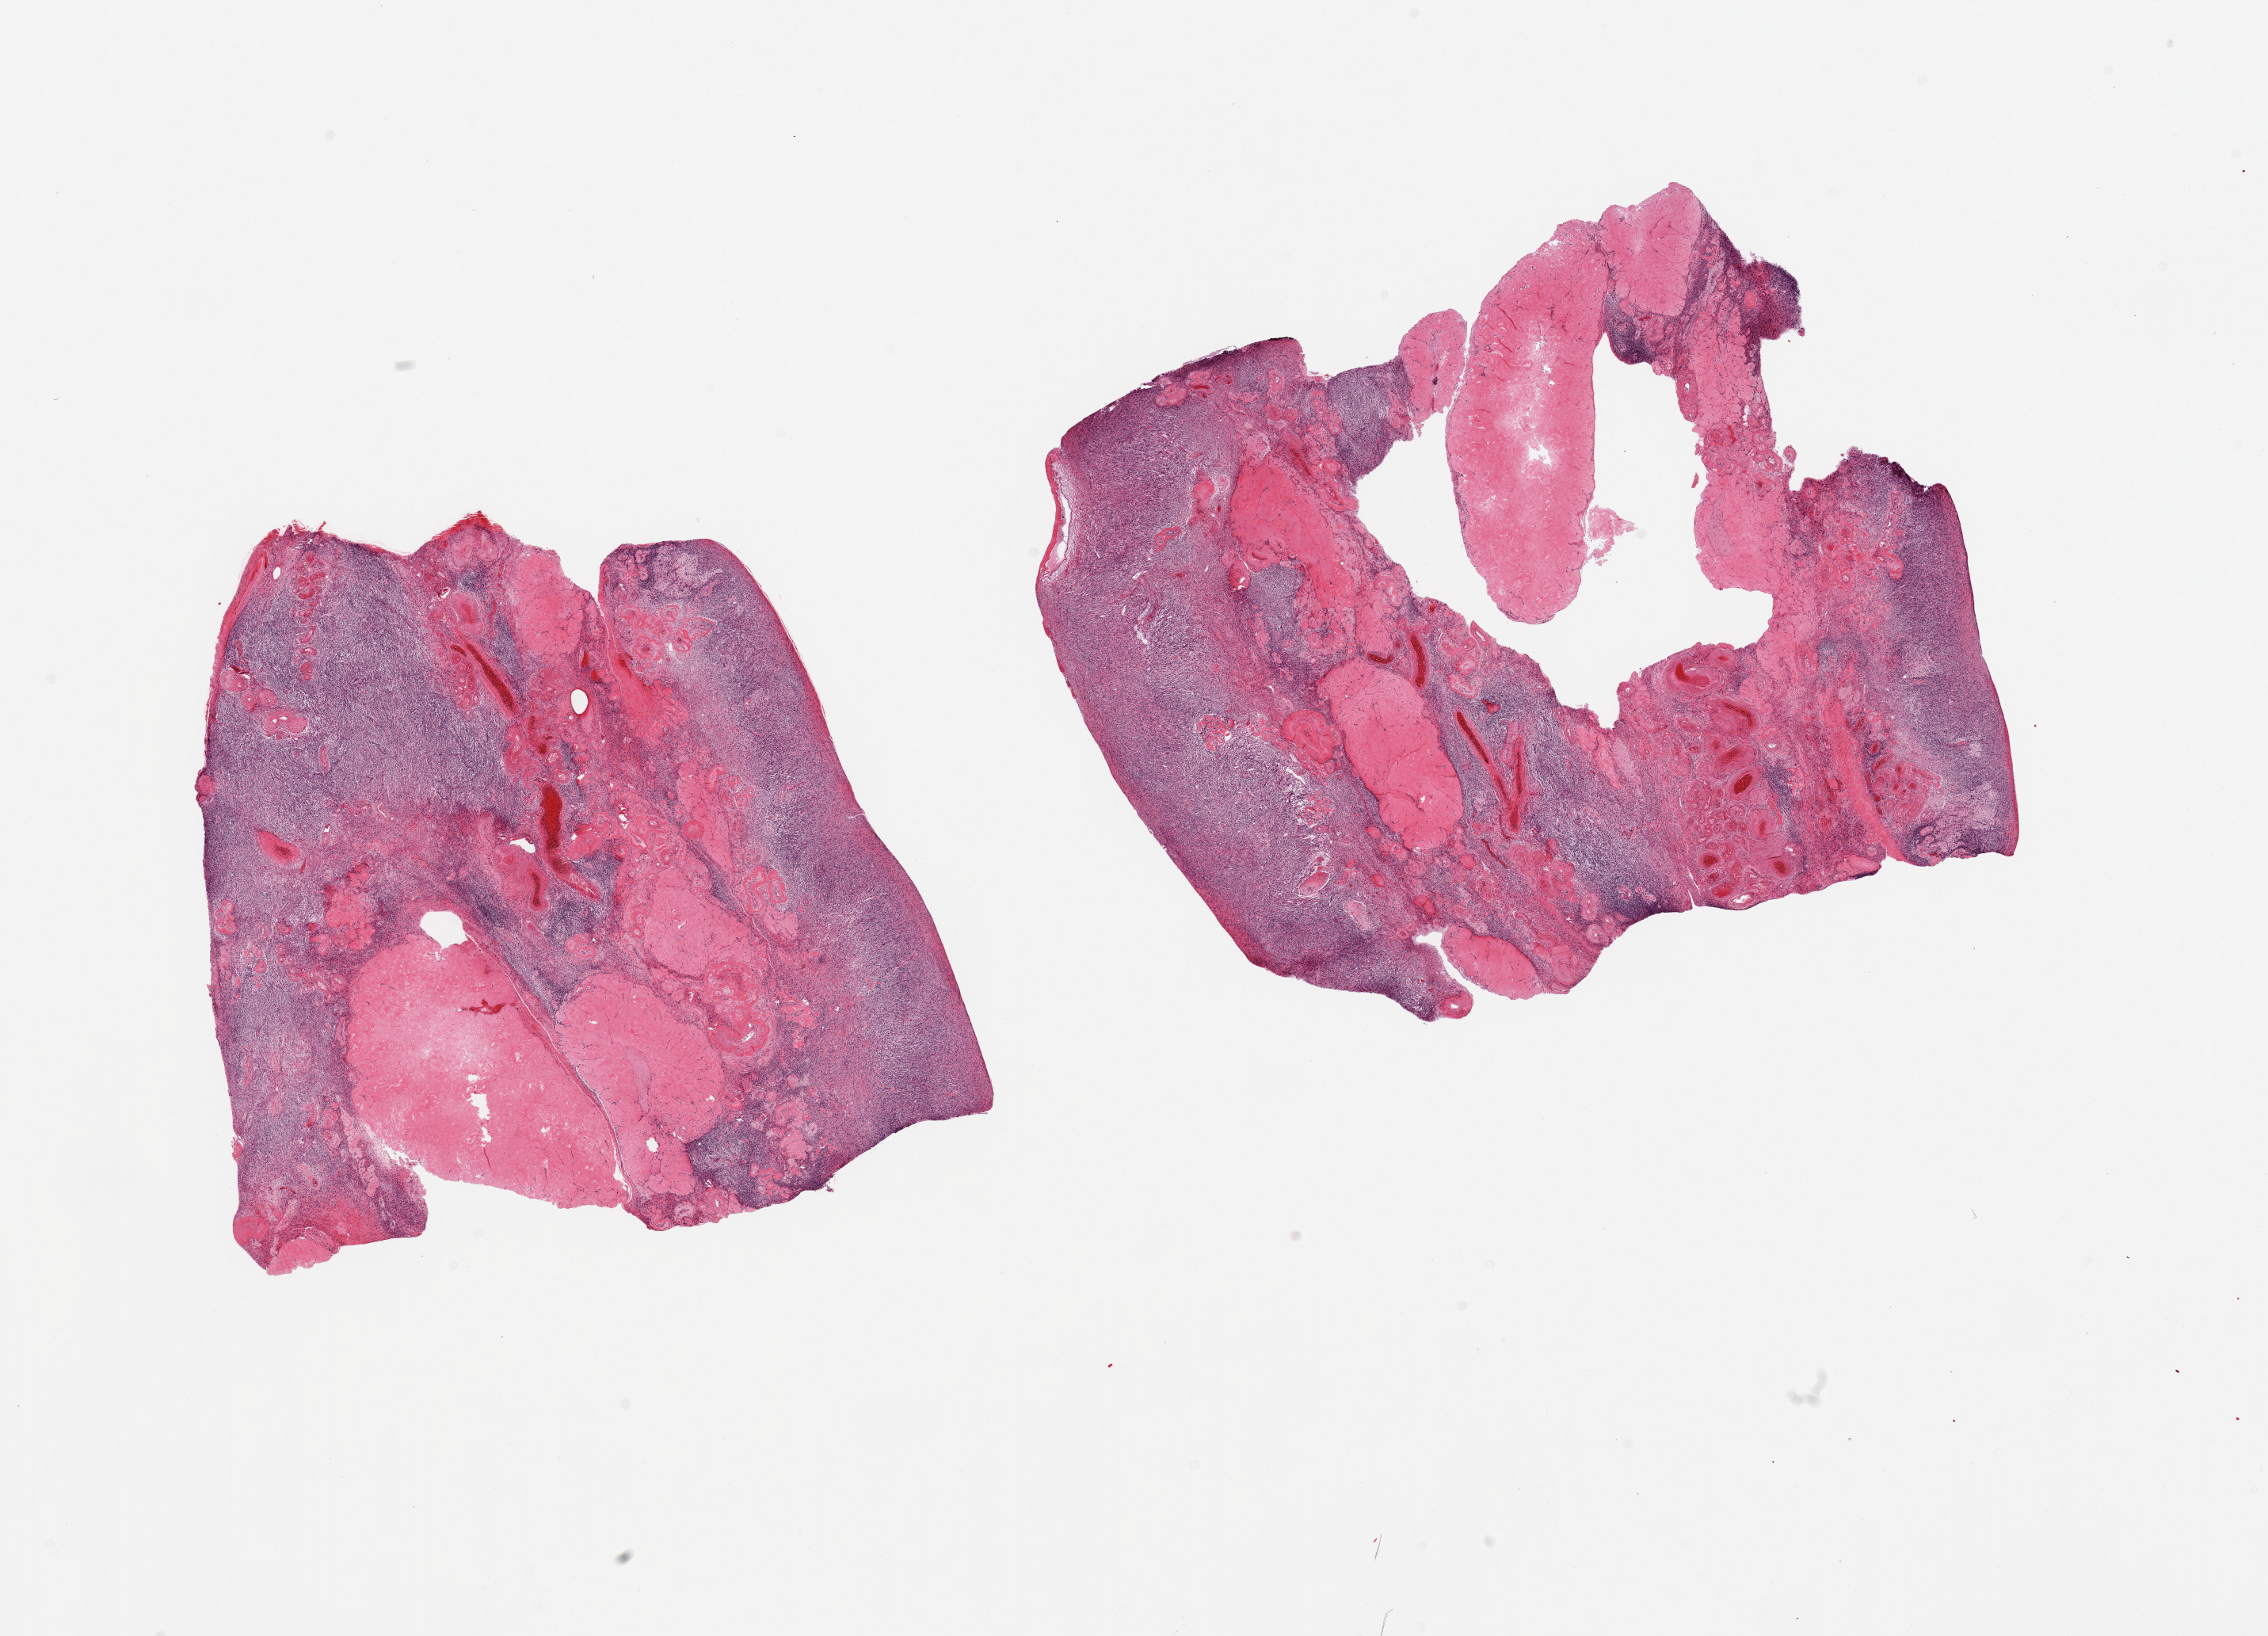
Digitized haematoxylin and eosin-stained section — a low-resolution overview of the entire scanned area, about 22.6 x 16.3 mm, PAXgene-fixed, paraffin-embedded tissue, sampled site (target tissue): ovary, donor tissue sample. Donor: female.
• pathologist's review note for this sample: 2 pieces; atrophic with corpora albicantia